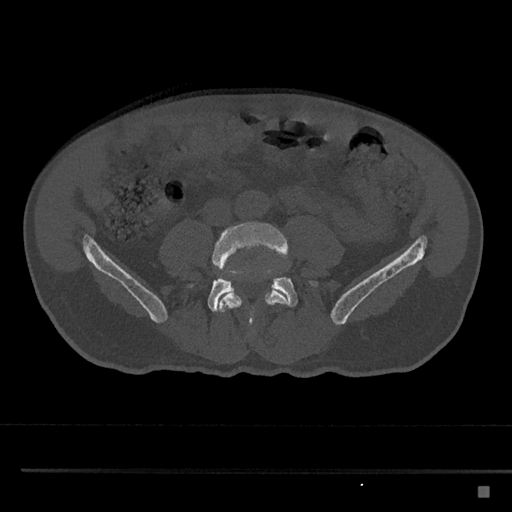
CT including the spine, one axial slice; position 608 of 797 along the scan axis; reconstruction kernel Br40s/3; bone window (W 1800 / L 400 HU); 512 × 512 image matrix. Male patient, age 59 years. Case-level facts recorded for this patient, not image findings: primary cancer: prostate.
Structures marked on this image (semi-automatically segmented with operator editing):
- L4 vertebra: bounding box [x1, y1, x2, y2] px = [212, 222, 289, 332]
- L5 vertebra: [186, 262, 319, 312]